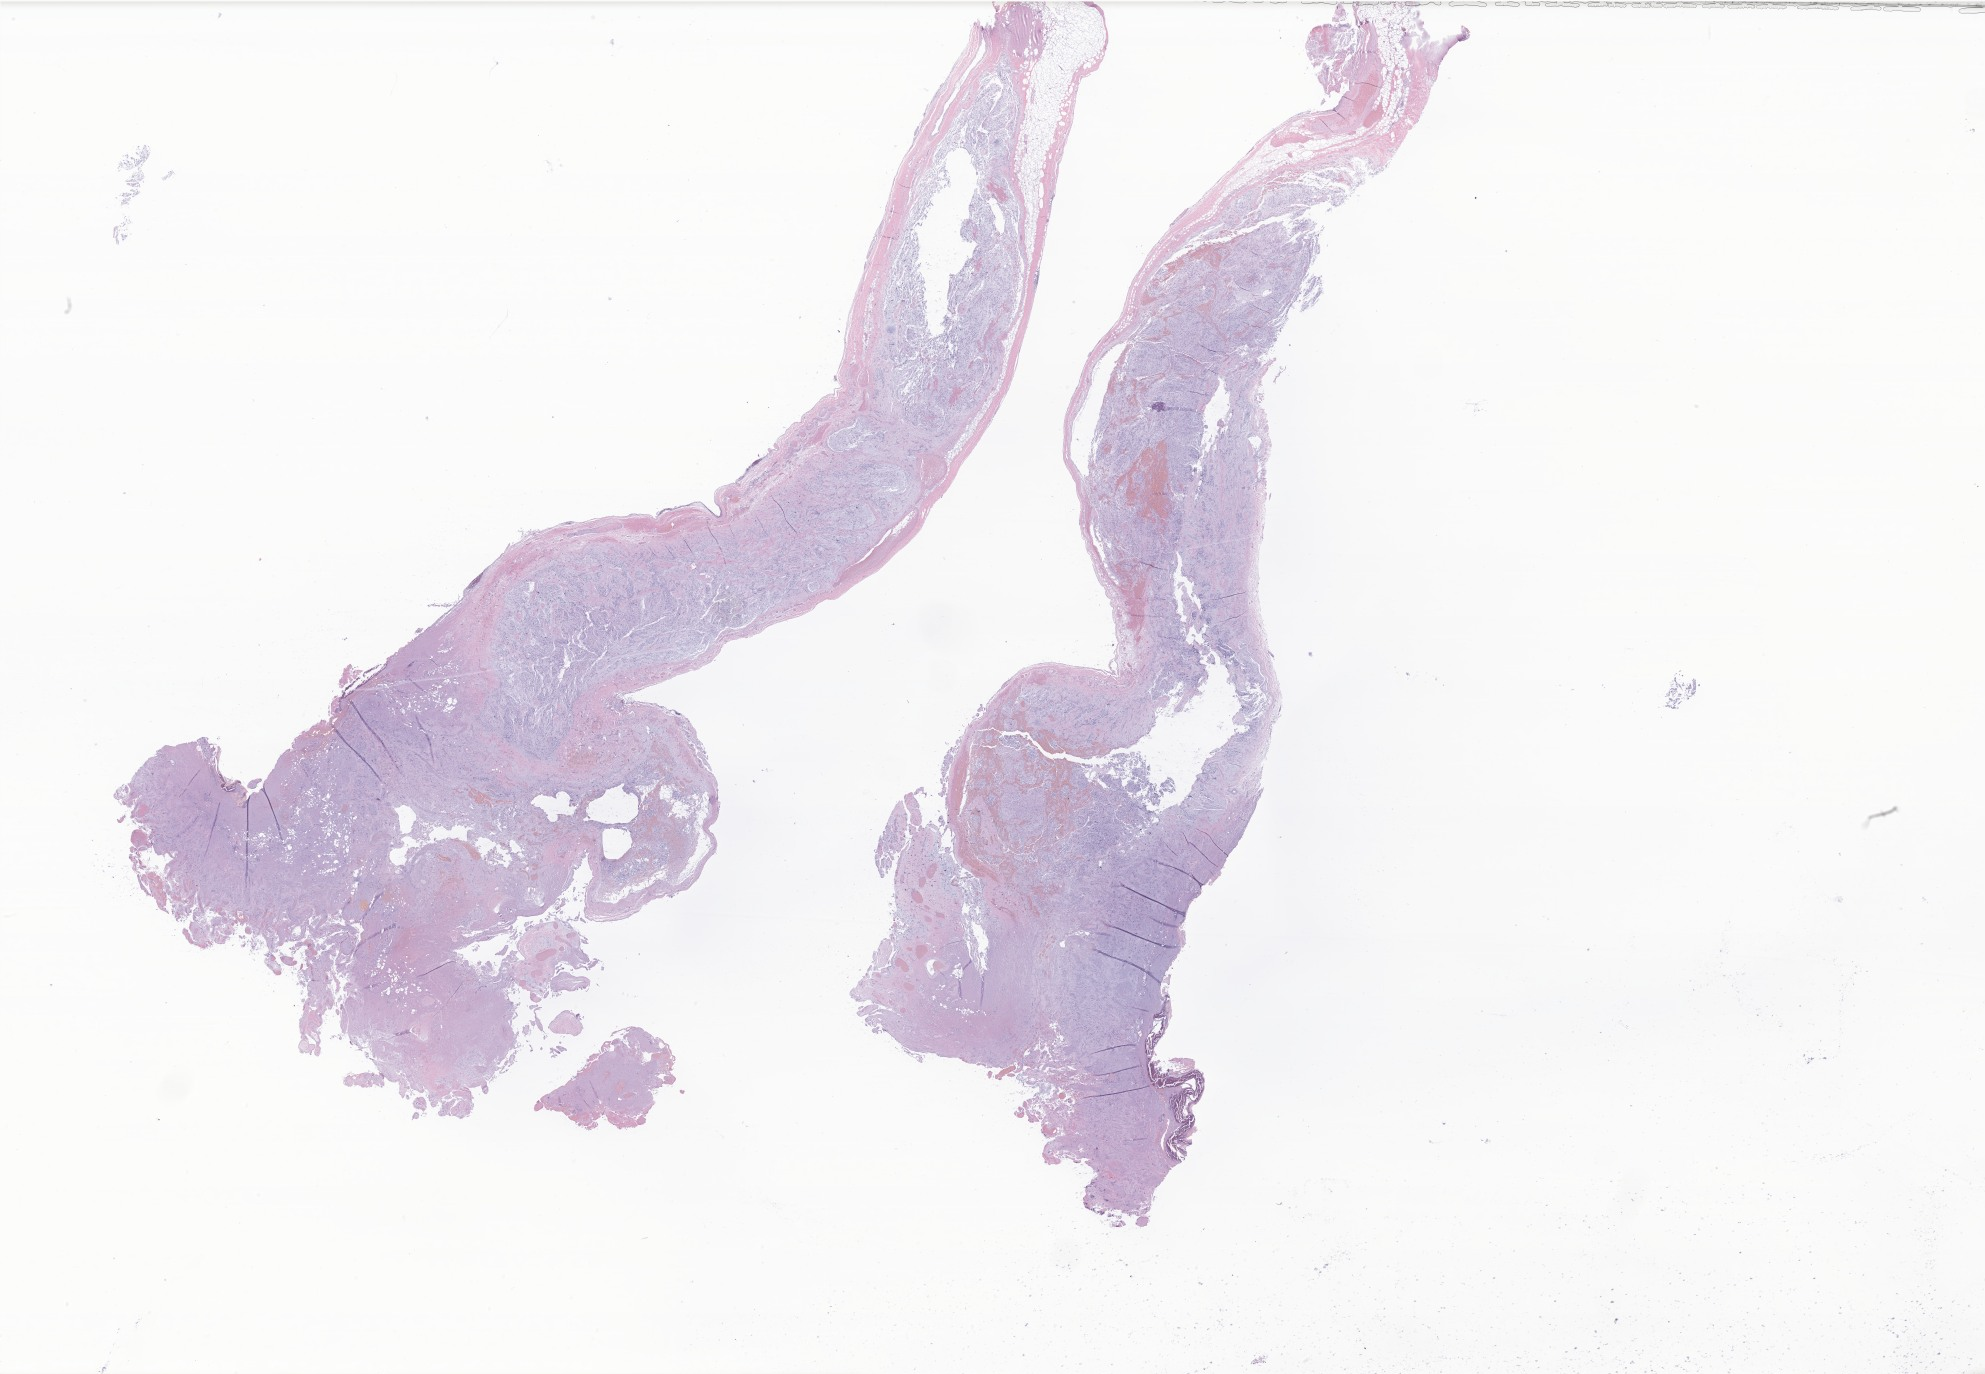
Haematoxylin and eosin whole-slide image of tumor tissue from the spinal cord — low-resolution overview of the scanned area, about 33.5 x 23.2 mm; FFPE section. Male patient, age 175 months.
Diagnosis (ICD-O-3 morphology term): Myxopapillary ependymoma.